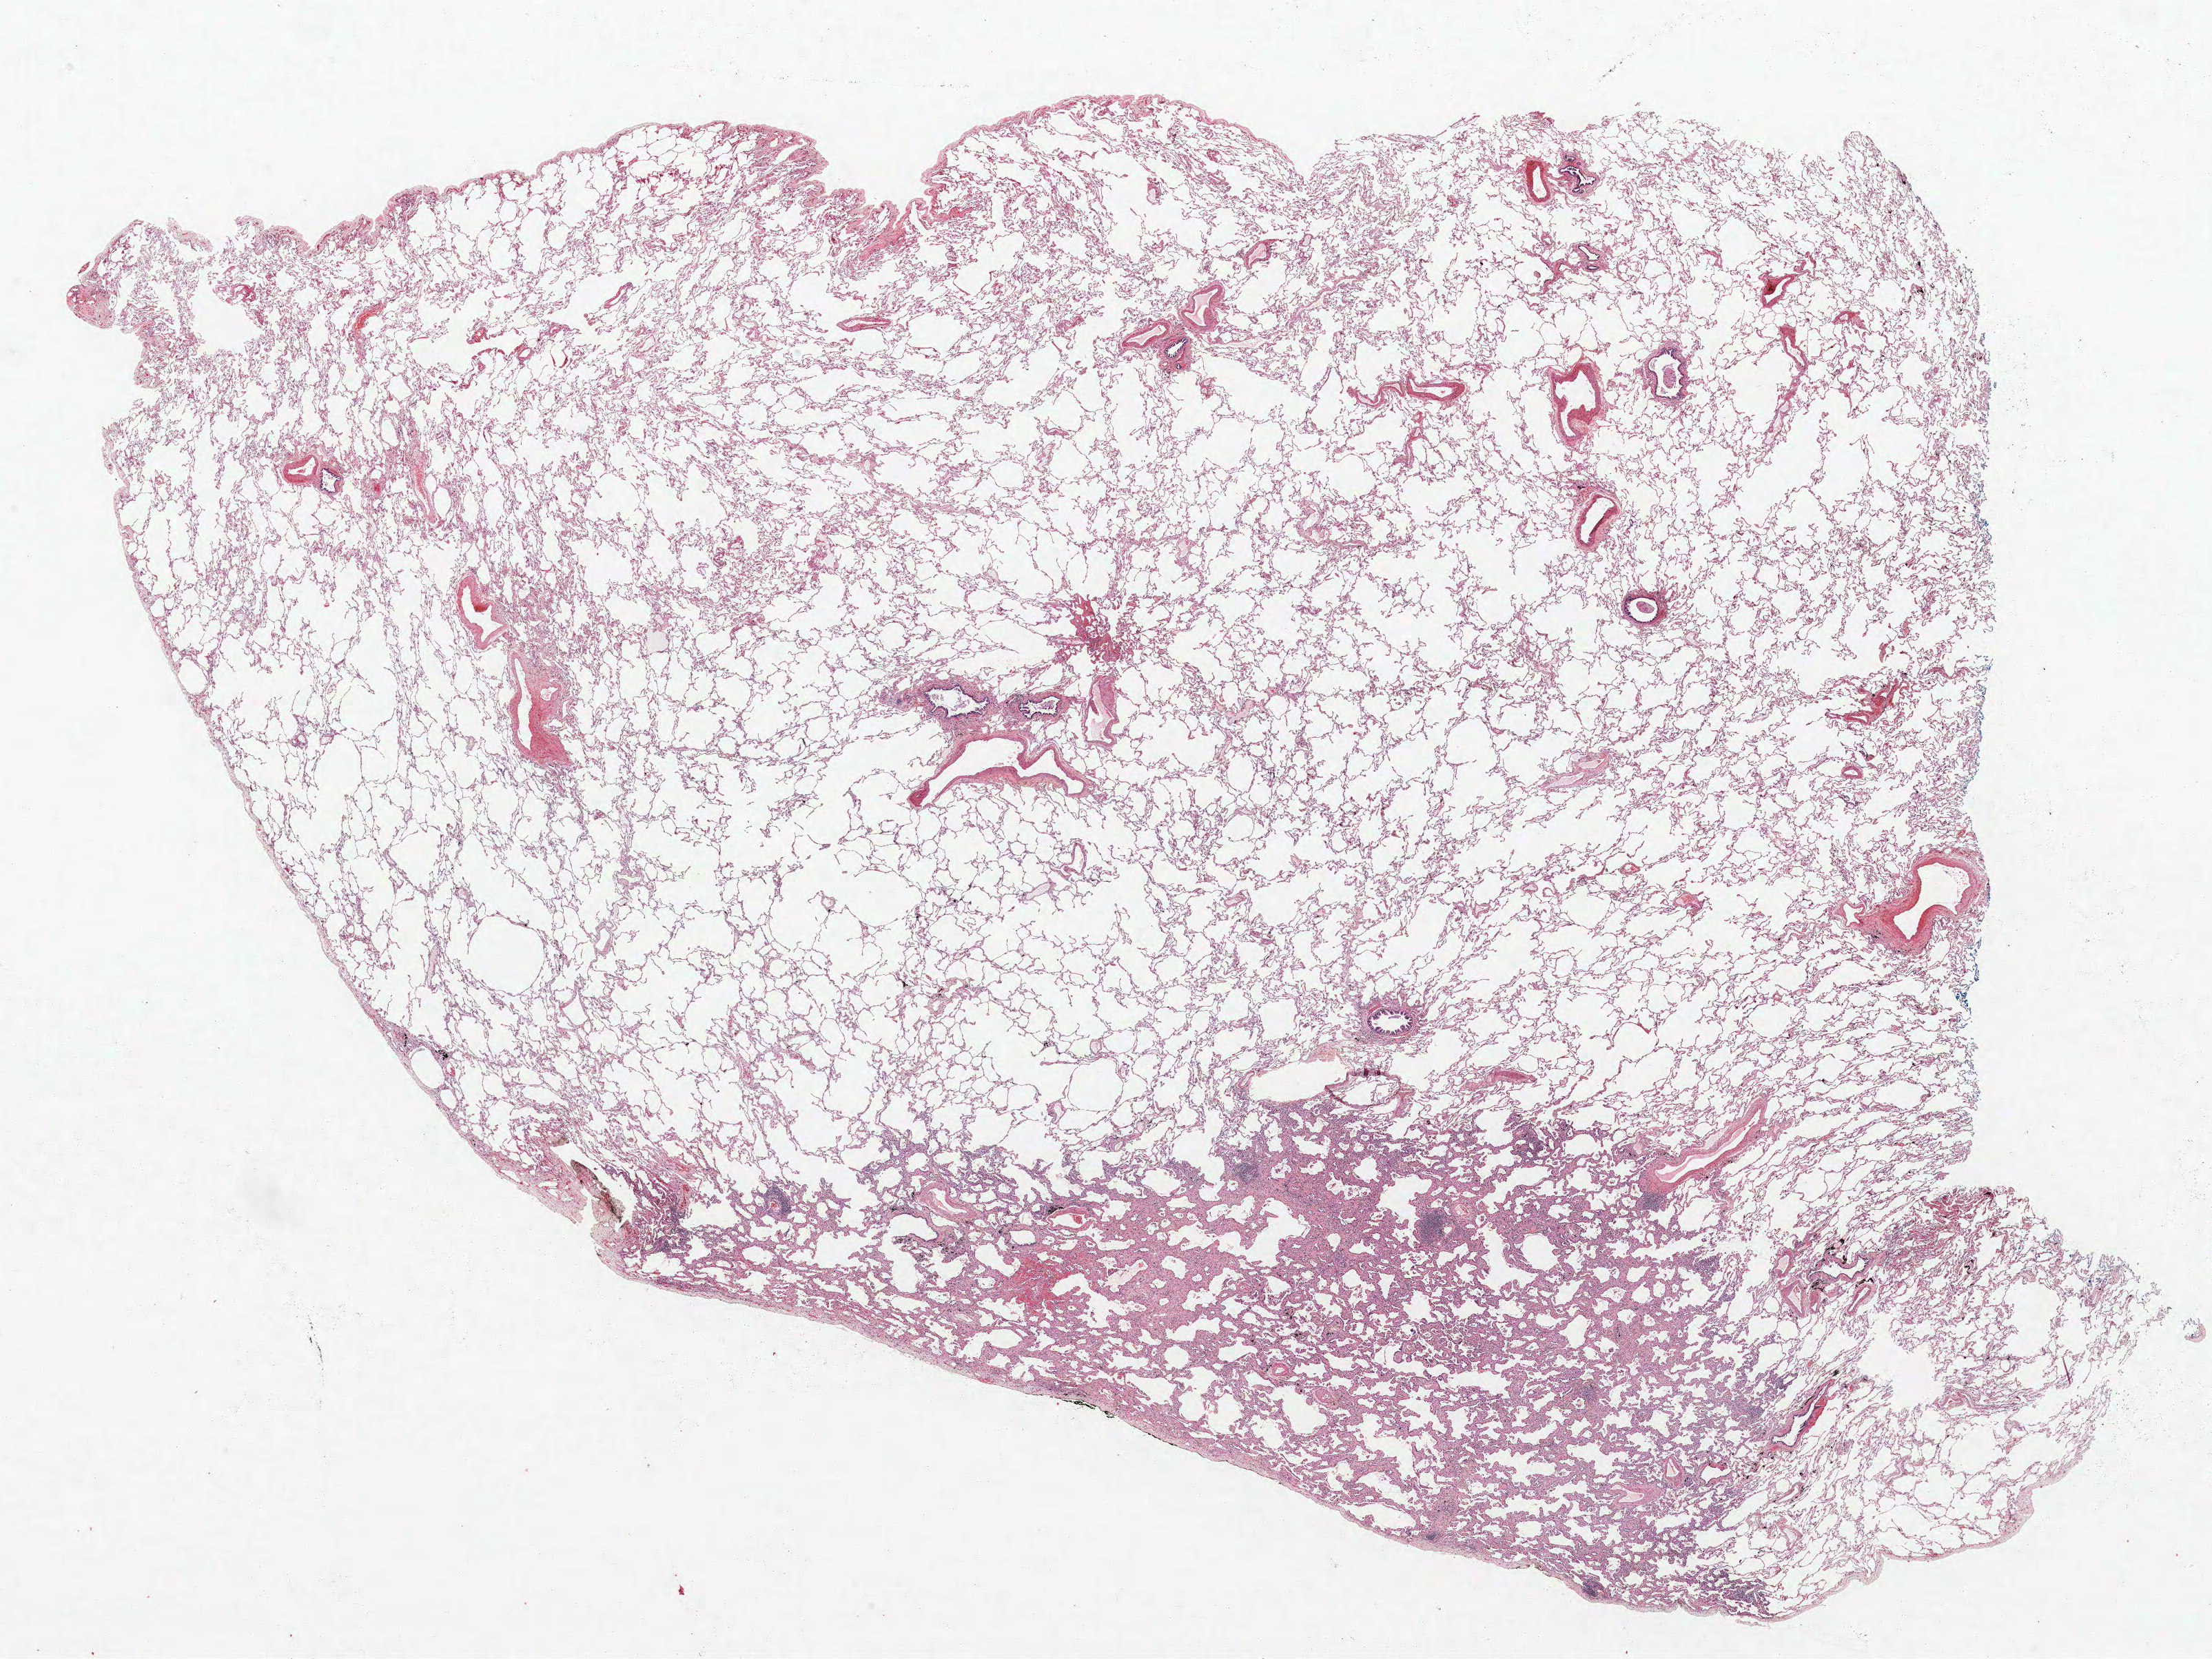
Hematoxylin and eosin (H&E) stained whole-slide image, a low-resolution overview of the entire scanned area, about 25.7 x 19.3 mm. FFPE section. Lung tissue. Female patient, aged 68 at enrolment. Grade: well differentiated (G1).
Primary tumour location (clinical record): right lower lobe. Stage (AJCC 6th edition): IA. Tumour size (pathology): 15 mm. Participant's lung-cancer diagnosis: Bronchiolo-alveolar adenocarcinoma, NOS.